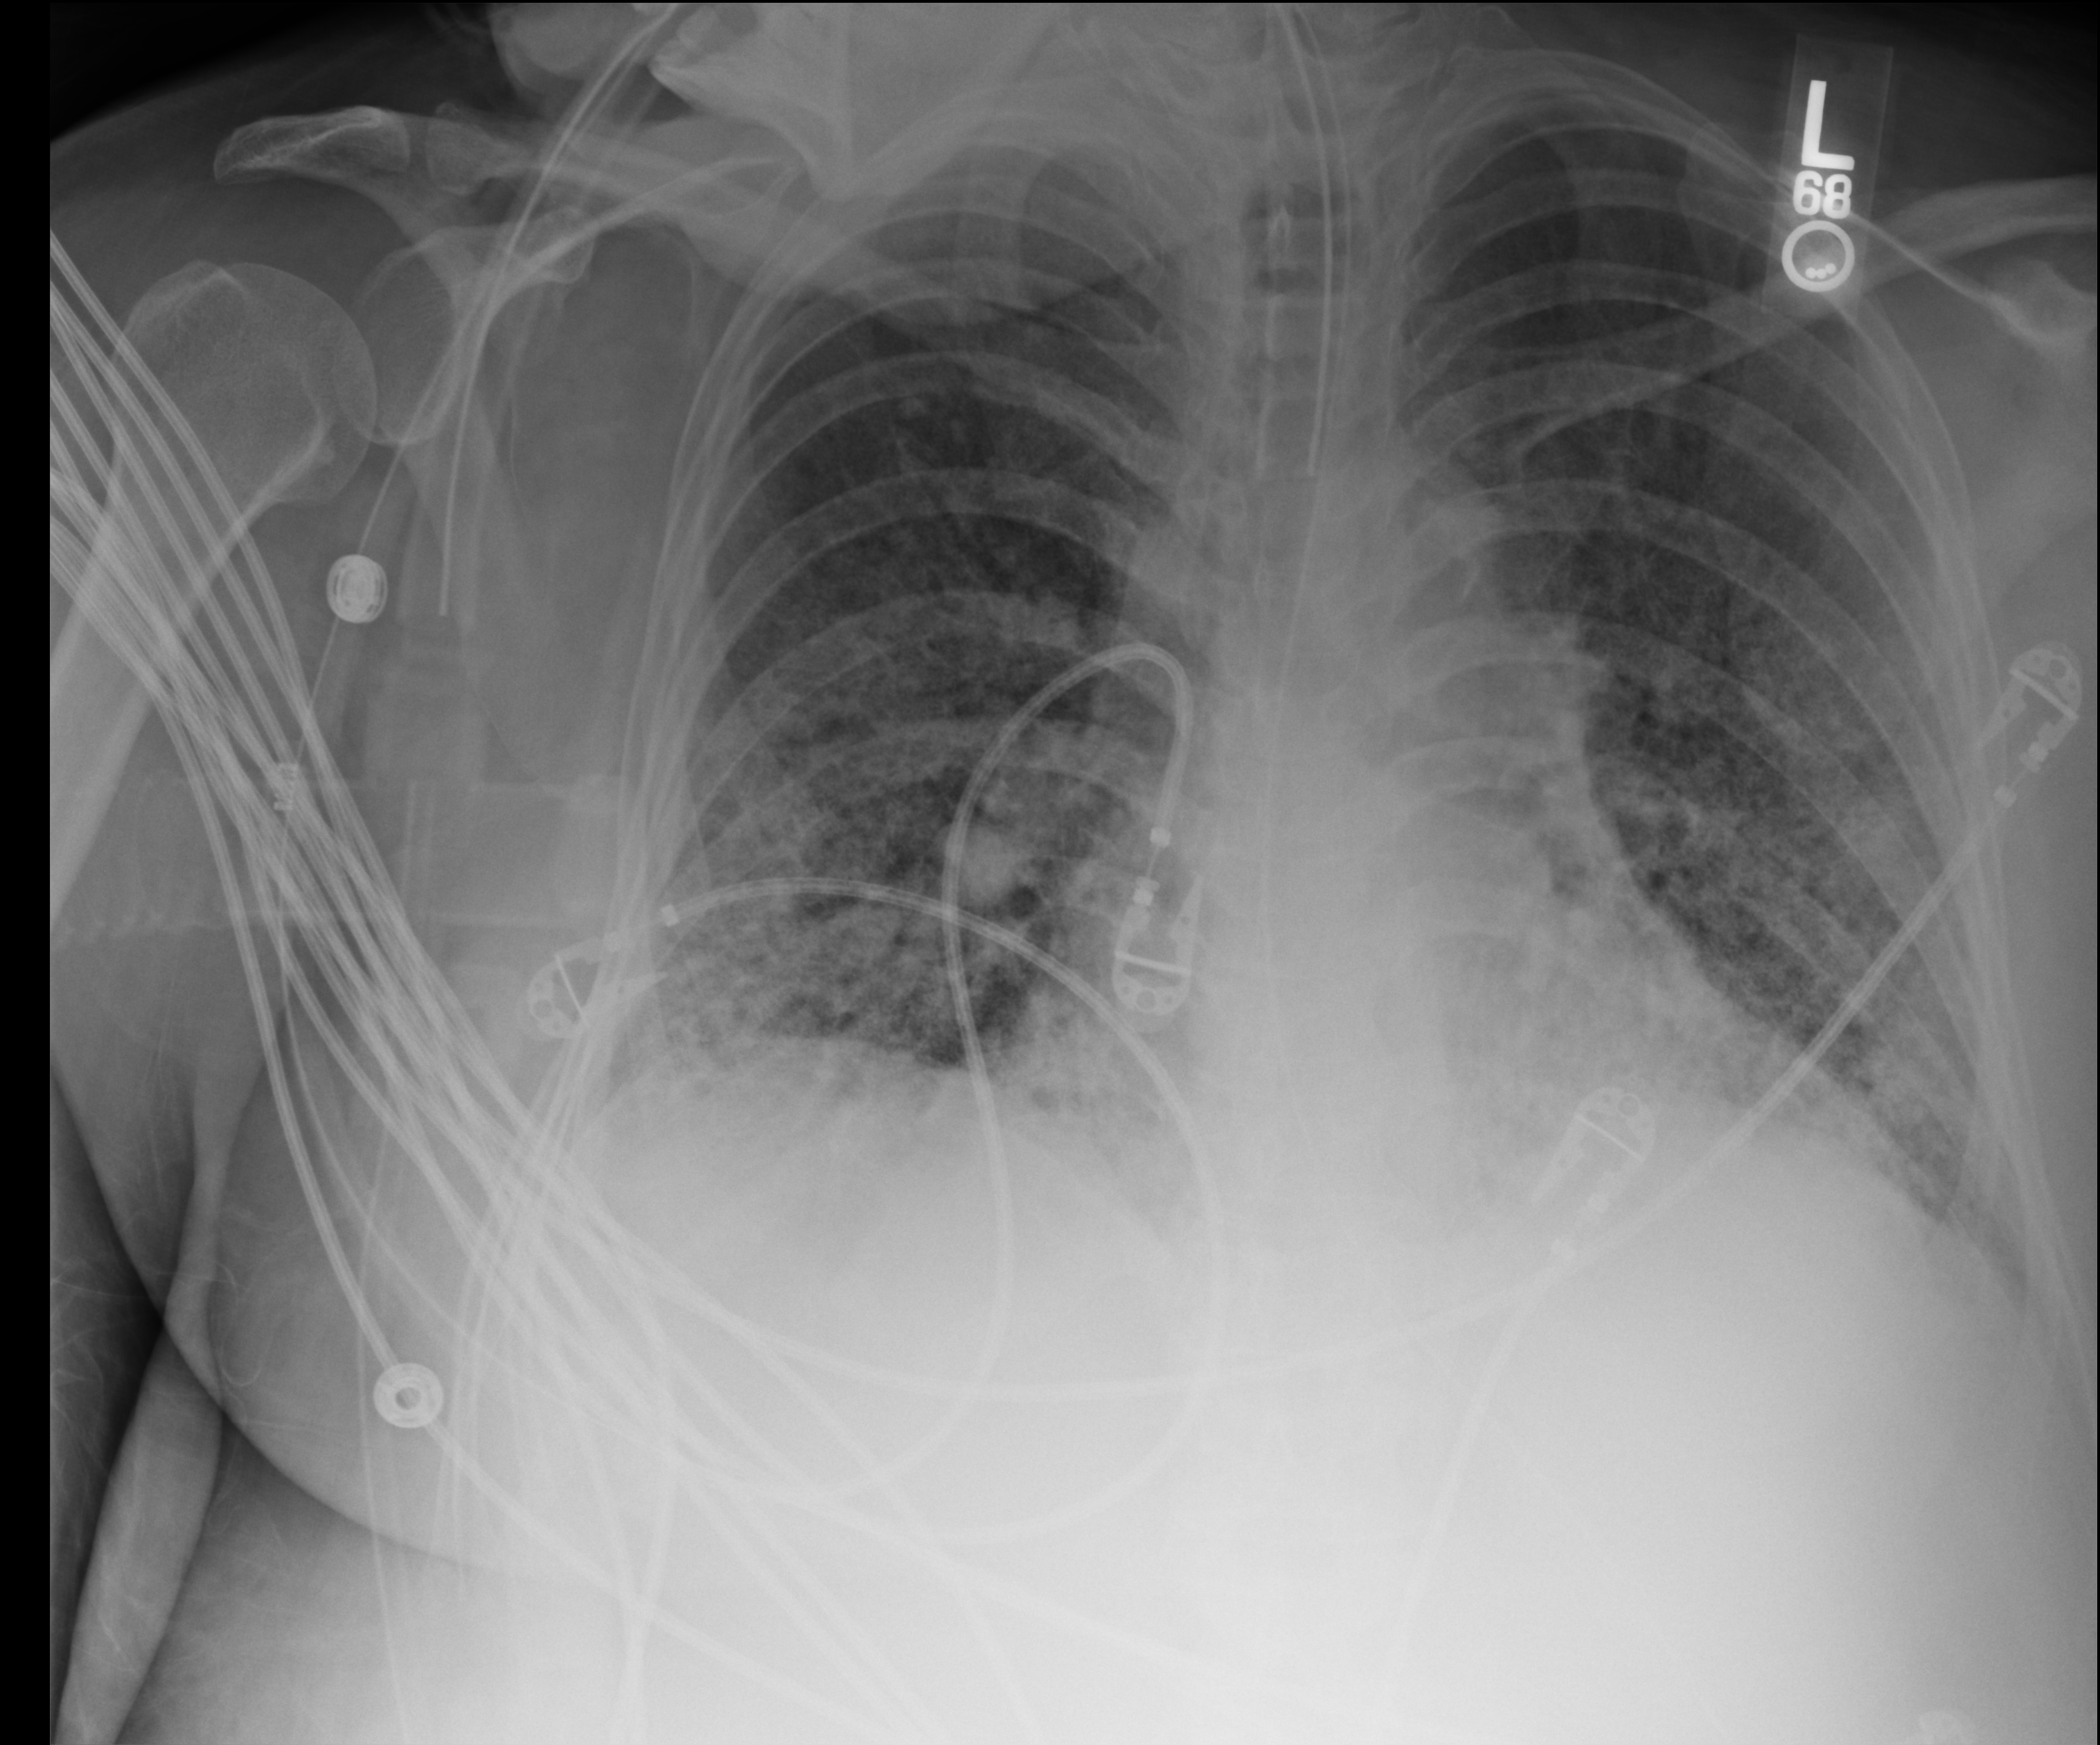
Bedside chest radiograph (computed radiography), anteroposterior (AP) projection. Patient hospitalised with COVID-19, aged 18–59 years.
From the hospital-stay record, not from the radiograph (when in the stay this image was taken is not recorded): smoking status (admission record): never.